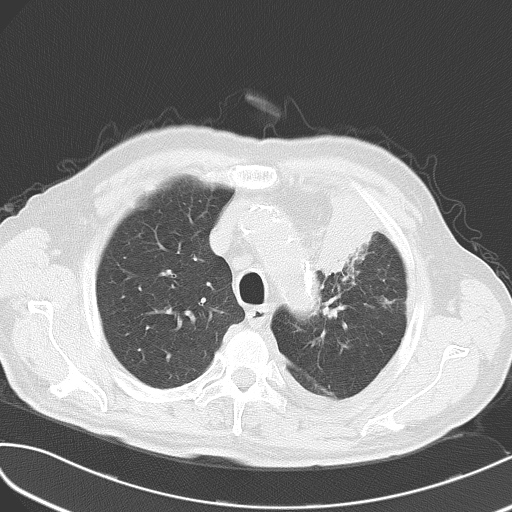
Chest CT, one axial slice; reconstruction kernel B70f; 120 kVp; lung window (W 1500 / L -600 HU); 5 mm slice thickness; 512 × 512 image matrix. Male patient, age 70 years. From the clinical record (not read from this slice): clinical TNM (as recorded): T2 N1 M3; histopathological grade: G3.
Structures marked on this image (rectangle marked by the reading radiologist):
- lung tumour (recorded histology: small cell carcinoma): bounding box <309,183,379,283> (left, top, right, bottom; pixels)